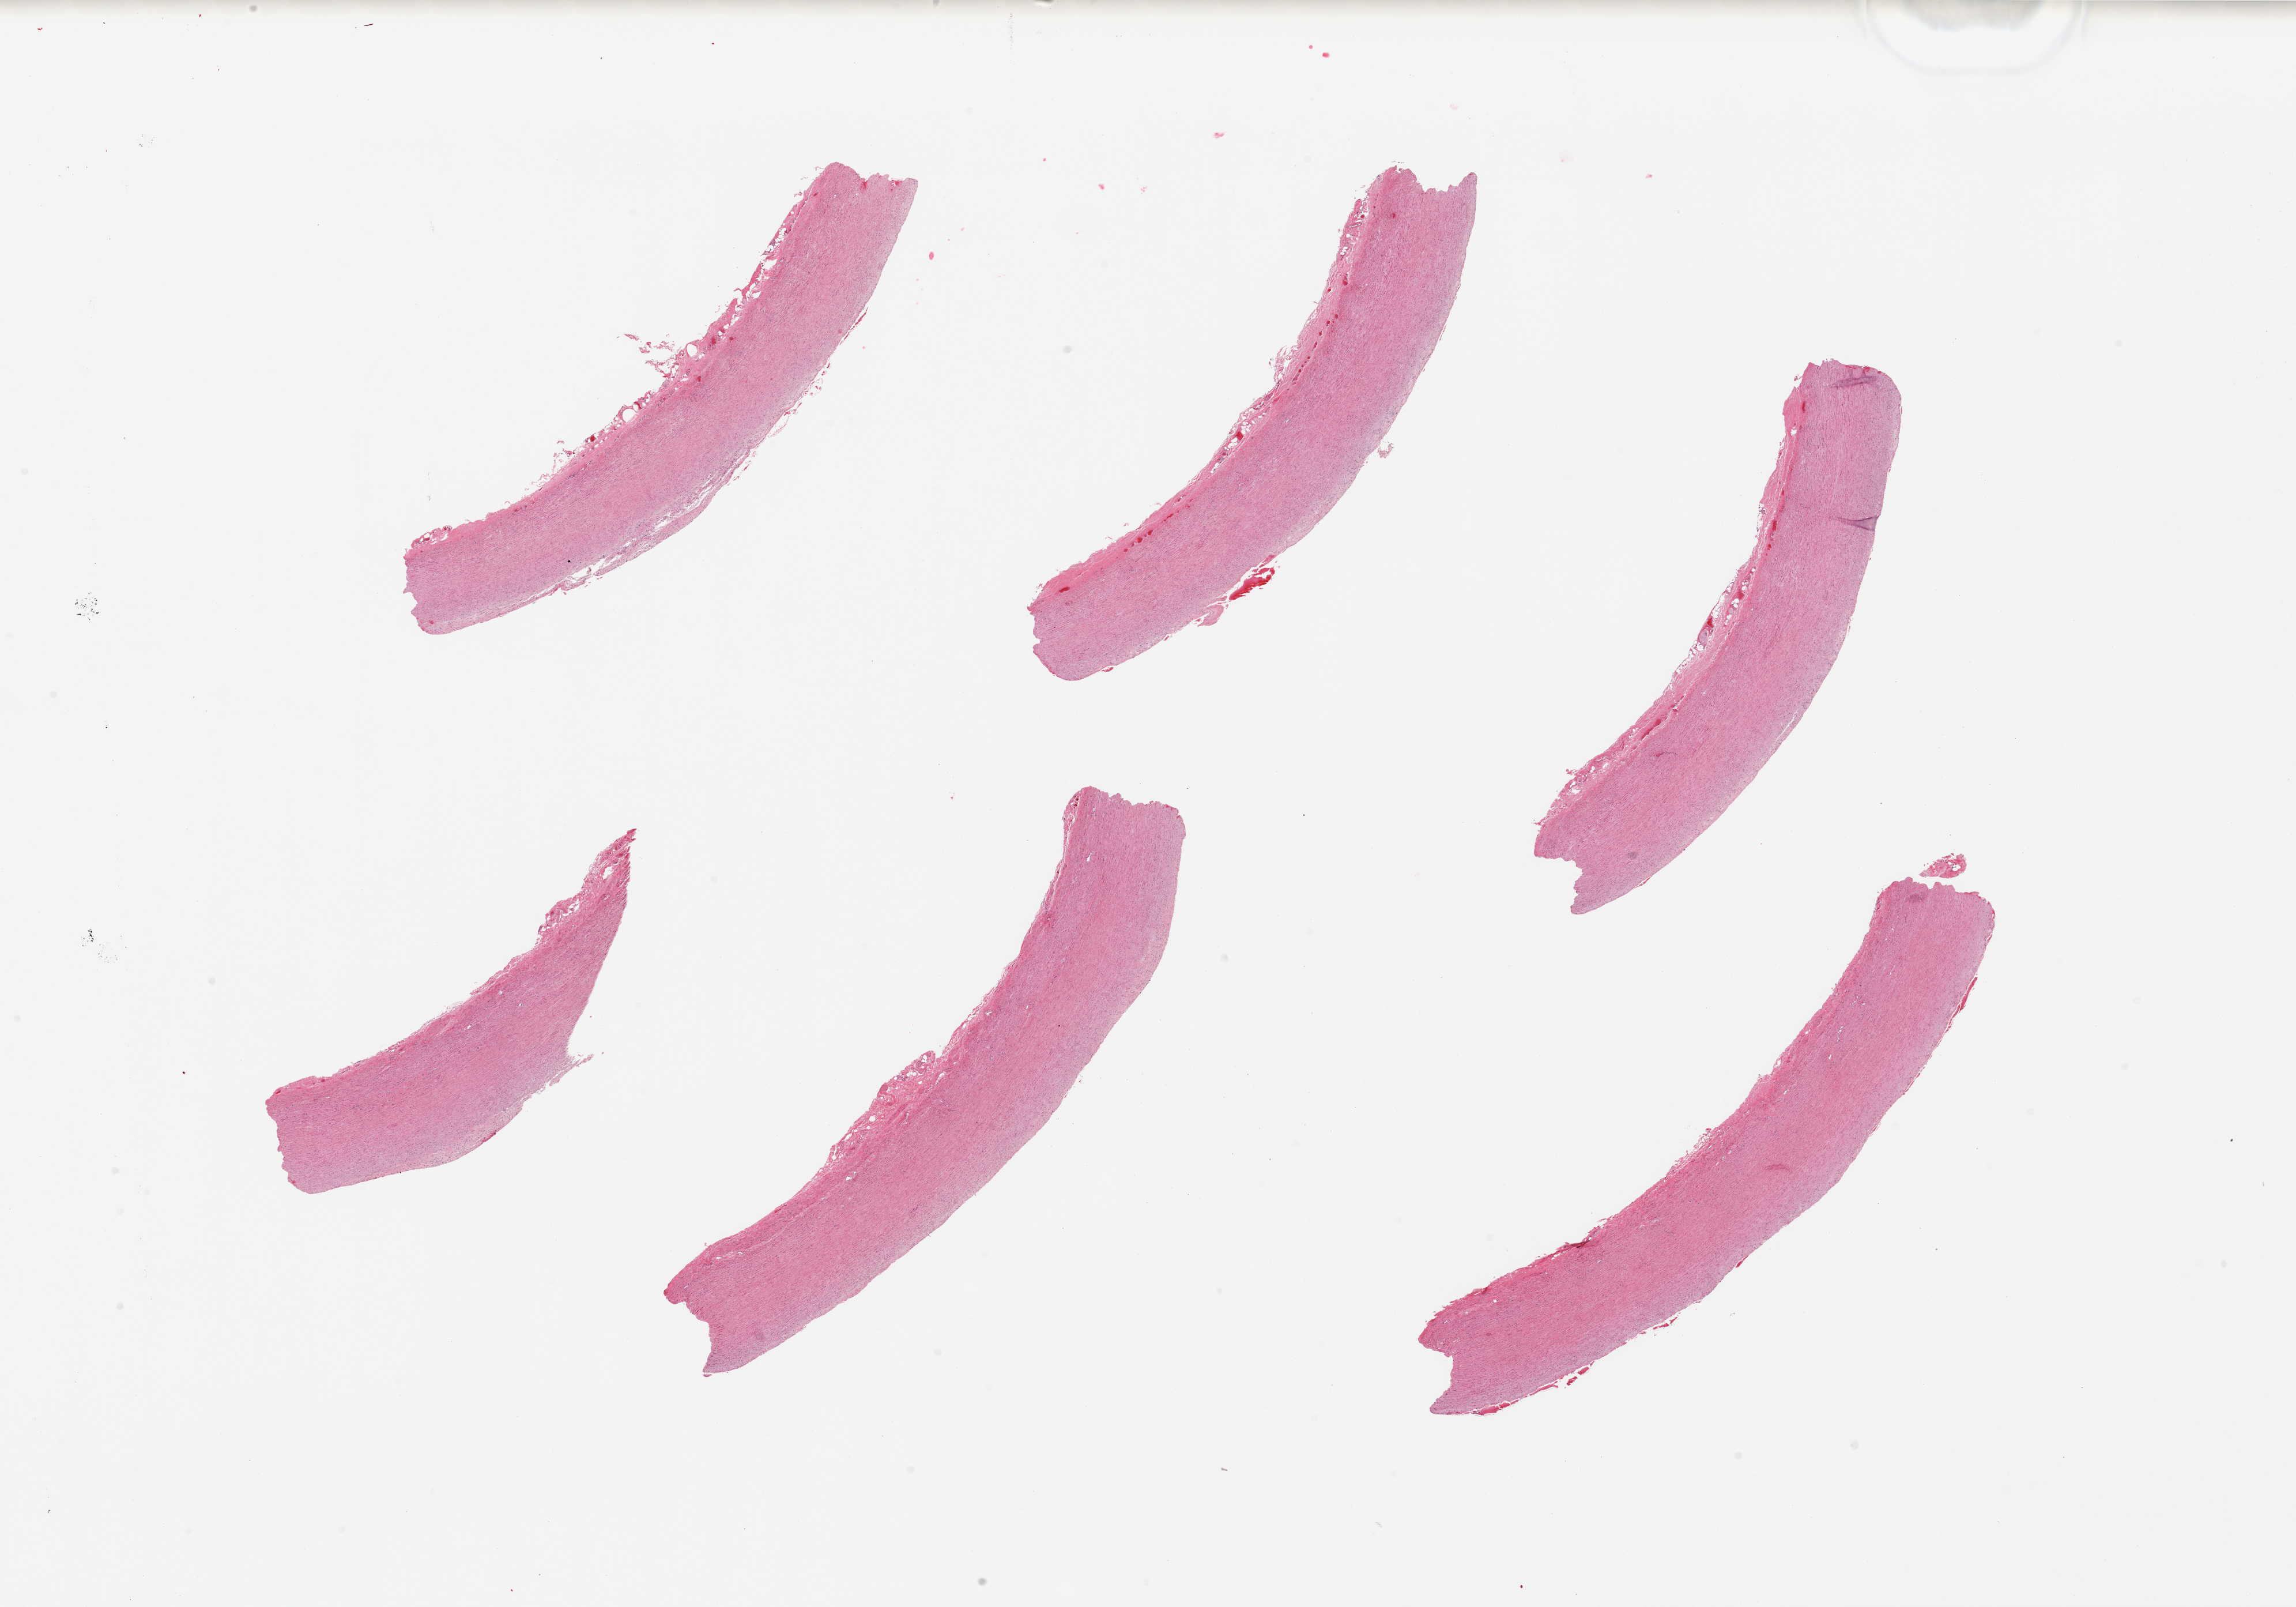
Whole-slide image, hematoxylin and eosin (H&E) stain — low-resolution overview of the scanned area, about 31.5 x 22.0 mm, PAXgene-fixed paraffin-embedded (PFPE) section, target tissue: aorta, donor tissue sample.
Pathologist's review note for this sample: 6 pieces; well trimmed; elastic degeneration.